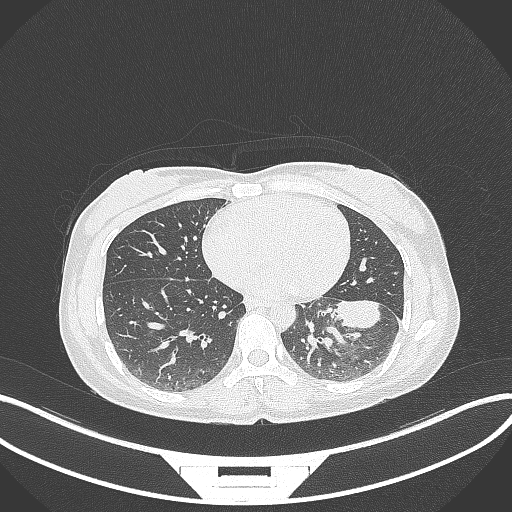
Chest CT, one axial slice. Slice 24 of 244 in the series (ordered by position). 120 kVp. Lung window (W 1500 / L -600 HU). 512 × 512 image matrix, field of view 400 × 400 mm. Patient: female, 41 years. From the clinical record (not read from this slice): clinical TNM (as recorded): T2a N3 M1b.
Outlined on this slice (rectangle marked by the reading radiologist):
- lung tumour (recorded histology: adenocarcinoma): bounding box [x1, y1, x2, y2] px = [333, 298, 393, 334]